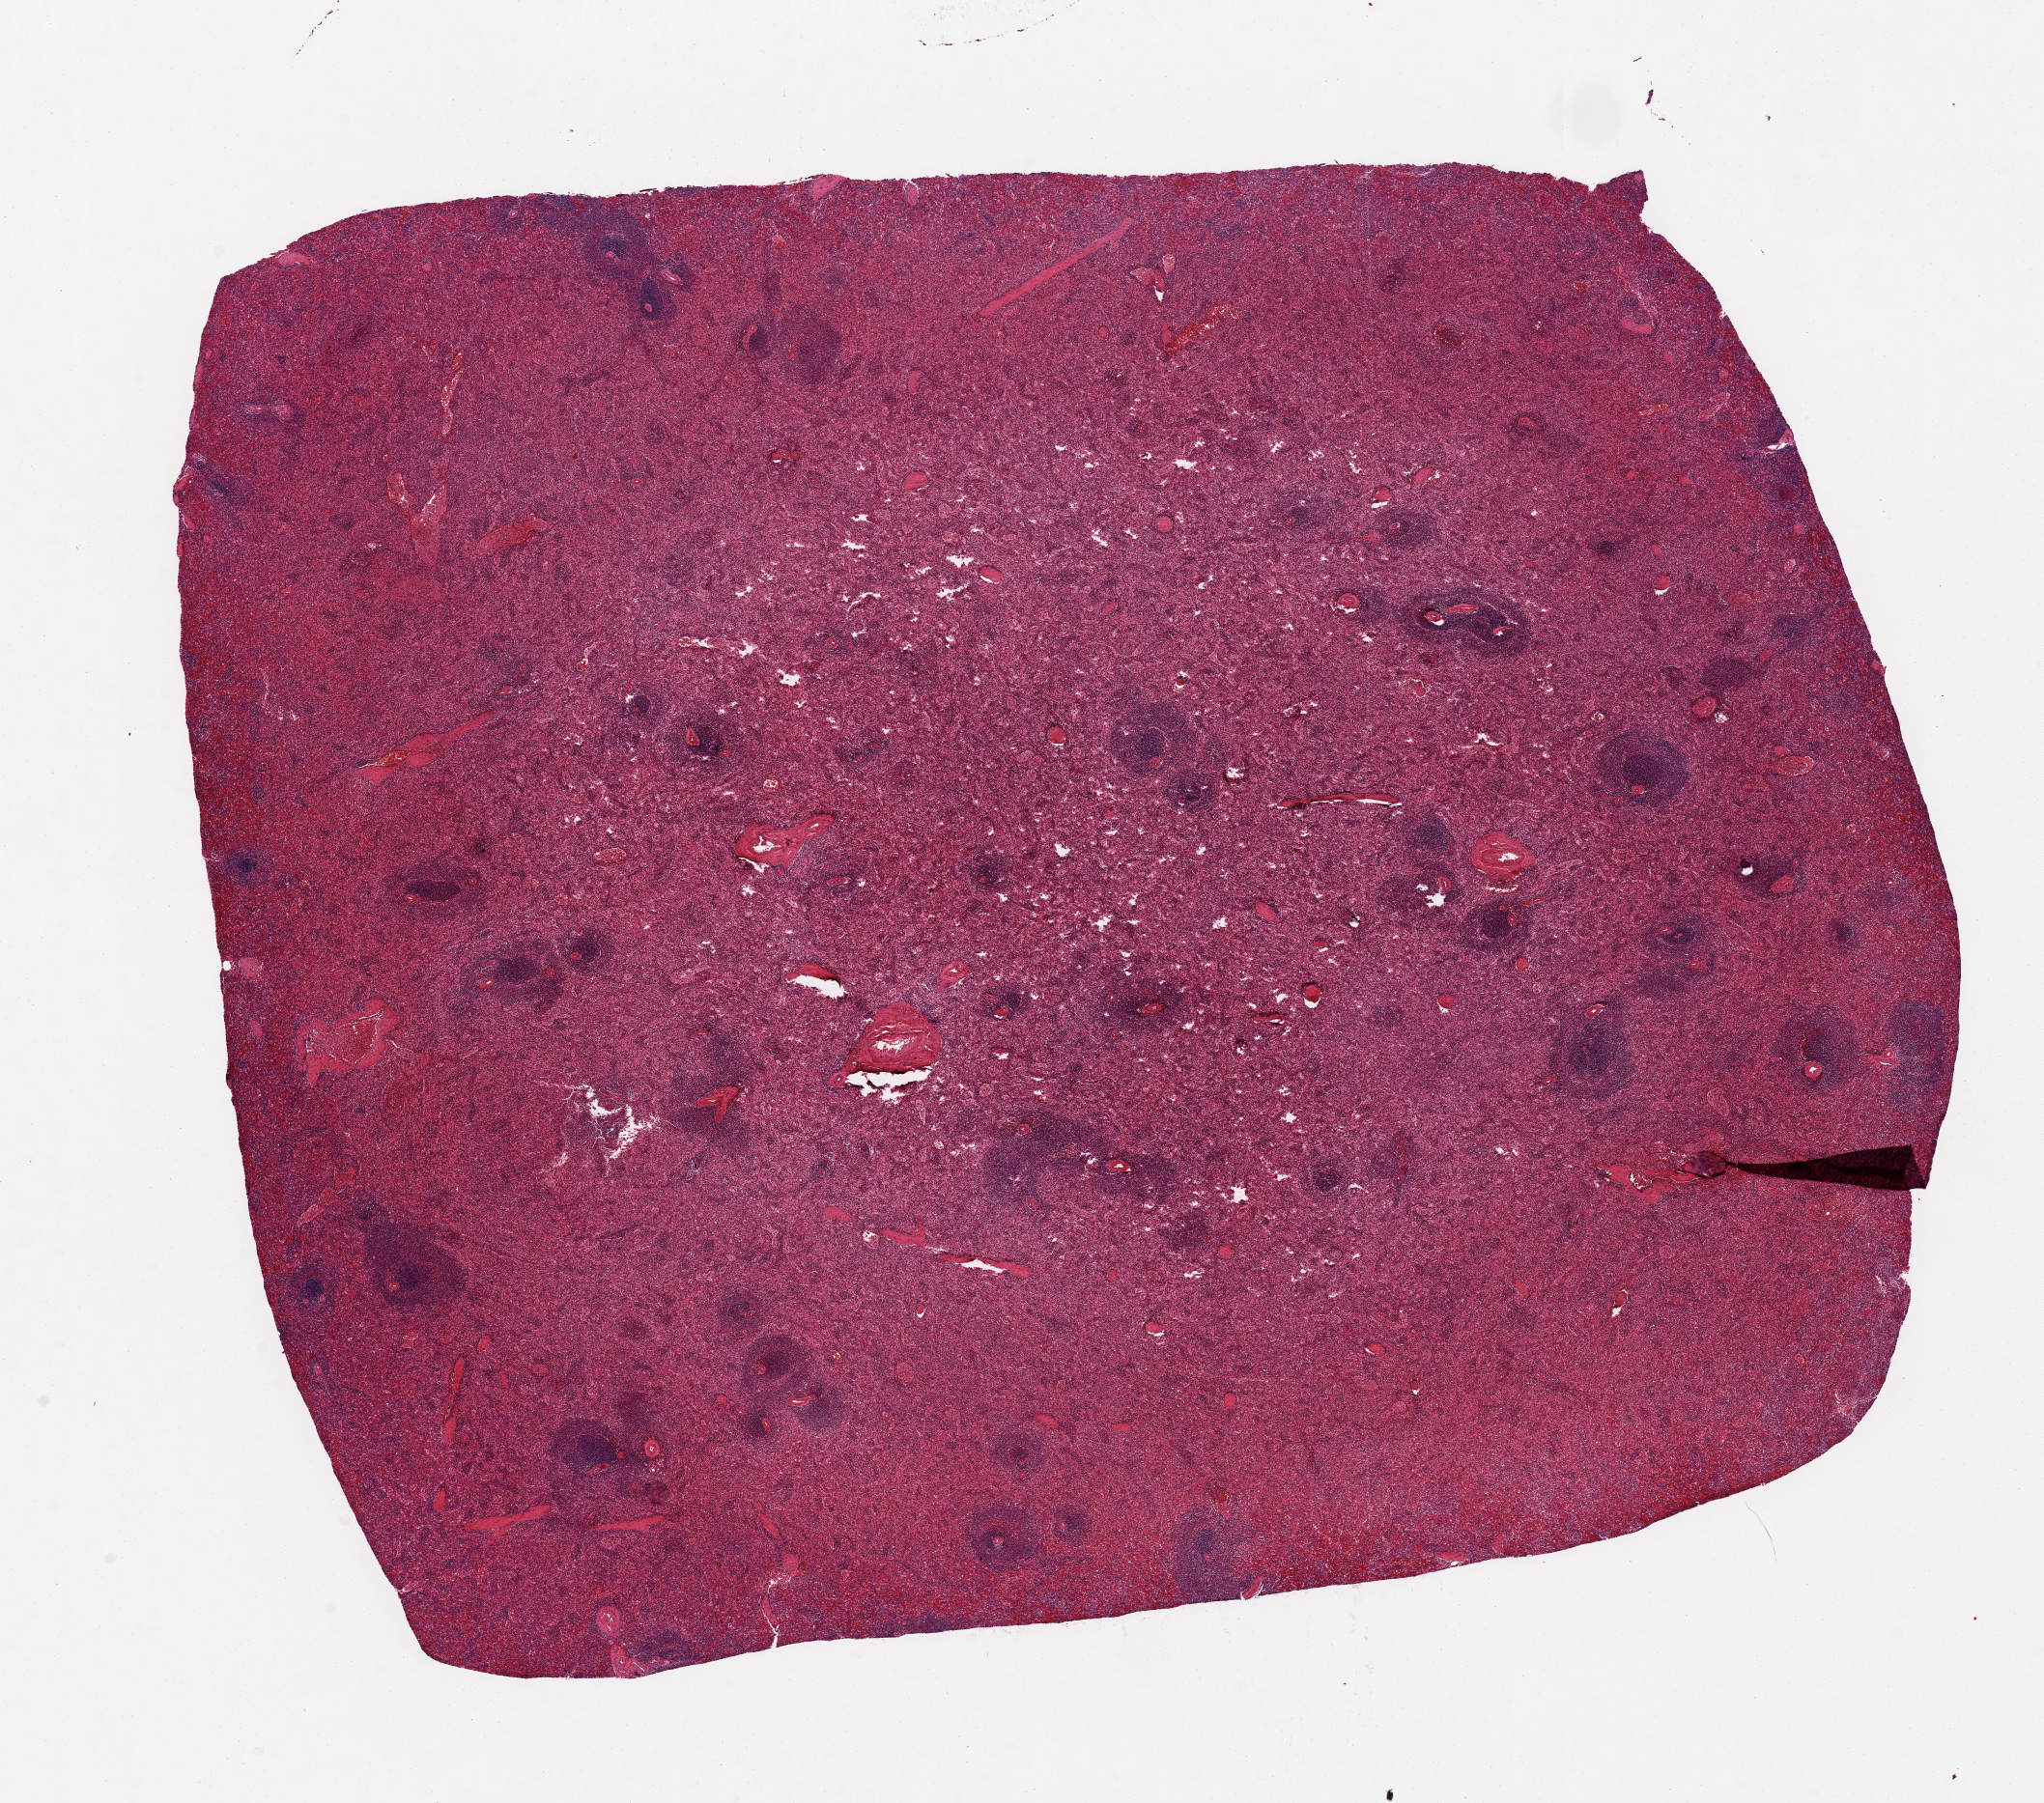
Digitized H&E-stained section — low-resolution overview of the scanned area, about 16.7 x 14.8 mm (acquisition: 20x scan); PAXgene-fixed paraffin-embedded (PFPE) section; target tissue: spleen; tissue donor sample. Donor: male.
• reviewer comment on this tissue sample: 1-2. 14x11.5mm. Central areas of poor fixation